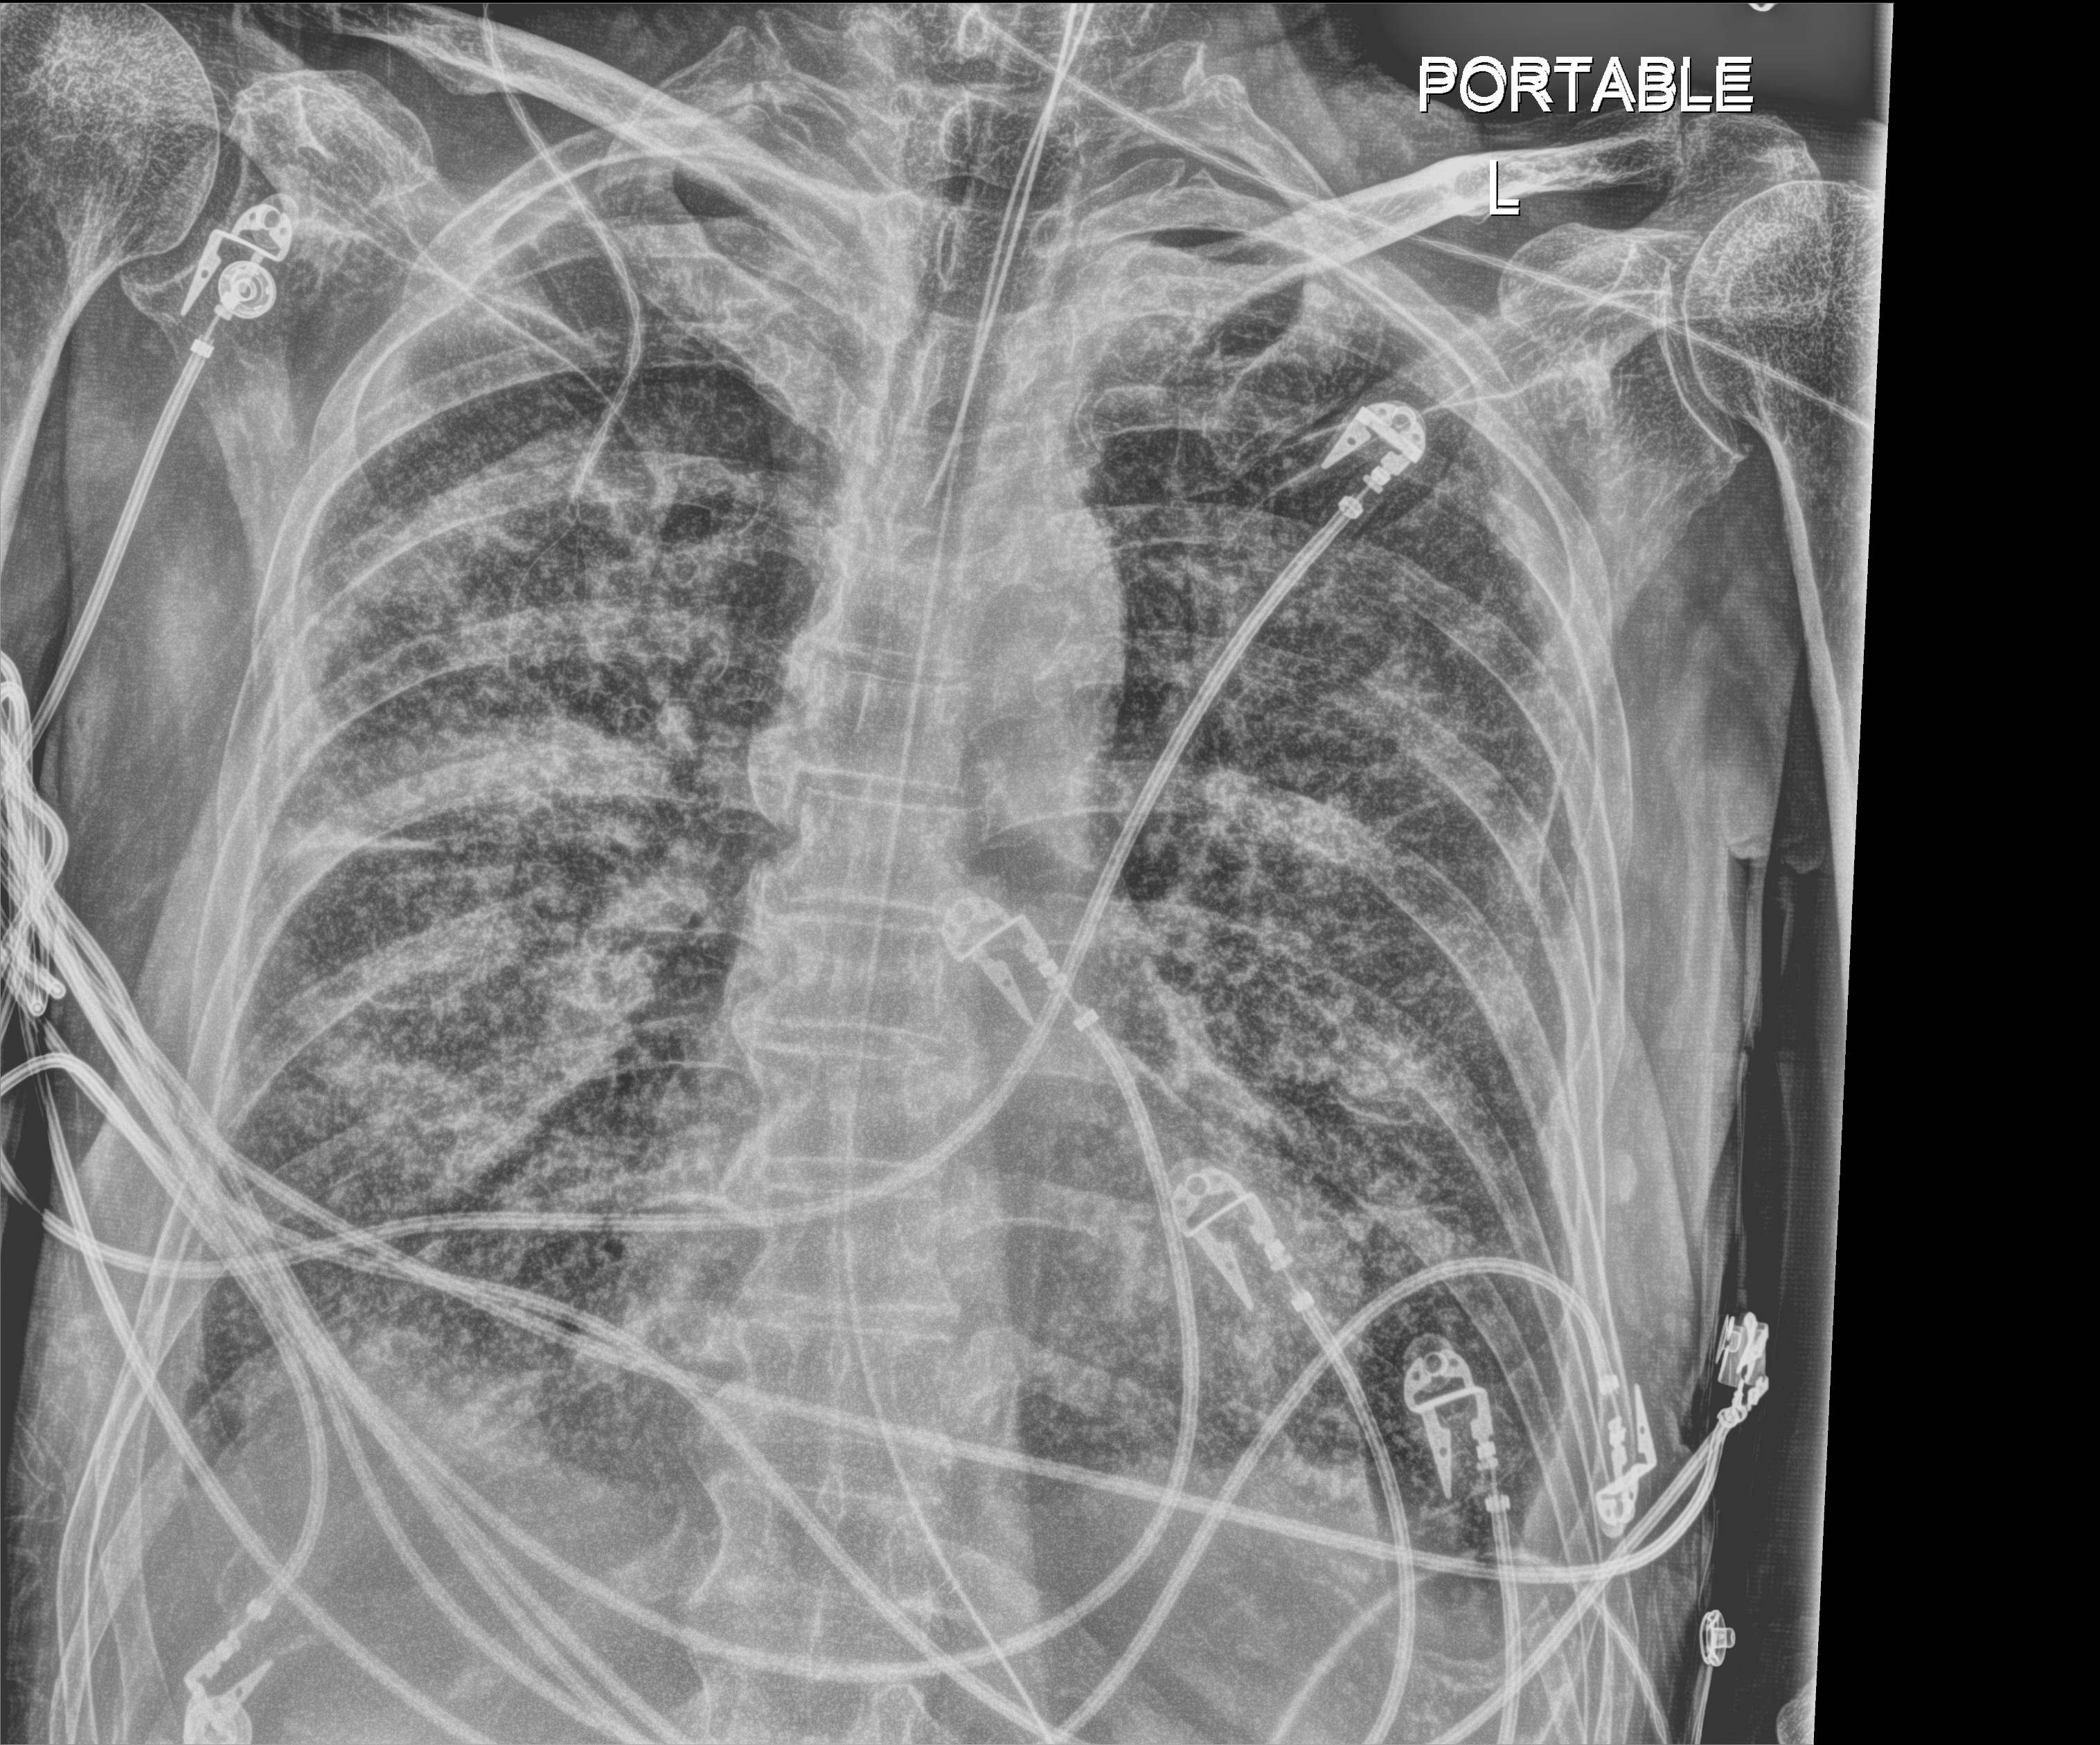
Portable chest radiograph. Patient hospitalised with COVID-19; male, aged 60–74 years.
From the hospital-stay record, not from the radiograph (when in the stay this image was taken is not recorded): admitted to intensive care during this hospital stay: yes; other chronic lung disease (admission record): no; mechanically ventilated during this hospital stay: yes.